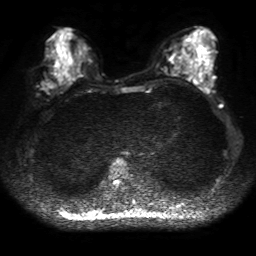
Breast MRI, one axial slice. Position 22 of 50 along the scan axis. Diffusion-weighted series; image 2 of 4 stored at this slice position (different b-values; order by instance number). 1.5 T. 256 × 256 image matrix. Female patient.
Annotated regions visible in this slice (expert manual segmentation):
- tumour on diffusion-weighted imaging: bounding box <41,79,56,91> (left, top, right, bottom; pixels)